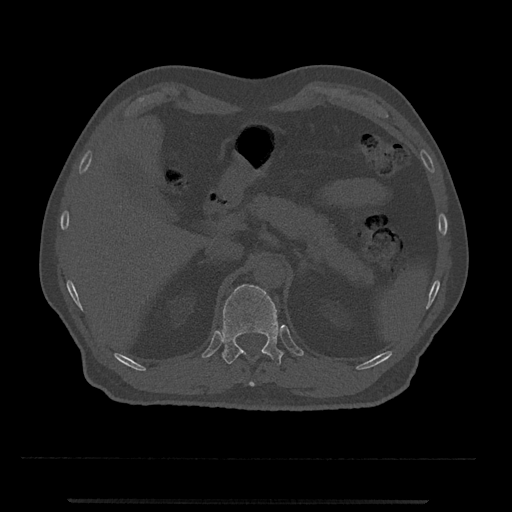
CT including the spine, one axial slice. Position 416 of 797 along the scan axis. Reconstruction kernel Br40s/3. Bone window (W 1800 / L 400 HU). 0.5 mm slice thickness. 512 × 512 image matrix, field of view 419 × 419 mm. Male patient, age 63 years. From the clinical record (not read from this slice): primary cancer: prostate.
Outlined on this slice (semi-automatically segmented with operator editing):
- T11 vertebra: bounding box [x1, y1, x2, y2] px = [239, 352, 269, 387]
- T12 vertebra: [222, 284, 284, 365]